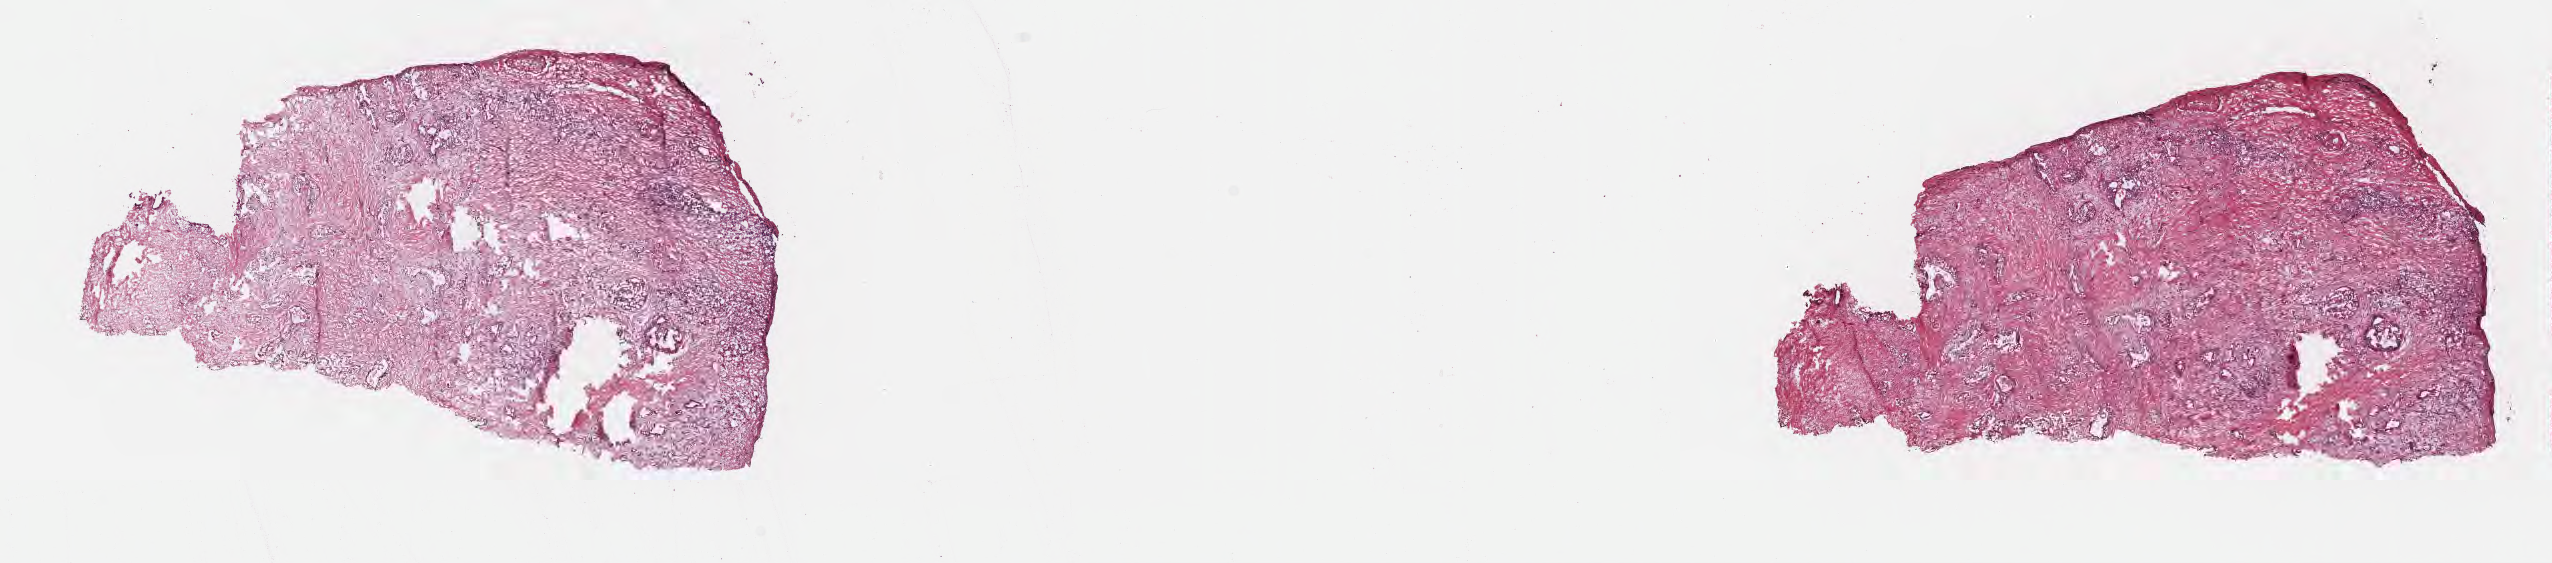
Whole-slide image, hematoxylin and eosin (H&E) stain, whole scanned area (about 20.6 x 4.6 mm) shown as a low-resolution overview, frozen section (tissue freezing medium), primary tumor, anatomic site: tail of pancreas. Female, age 63 years at initial diagnosis. Tumor grade: G2 (moderately differentiated). Composition of this section per pathologist review: tumor cells 20%, tumor nuclei 25%, stromal cells 80%, necrosis 0%, normal cells 0%. Inflammatory infiltration, as recorded: lymphocyte infiltration 0%, monocyte infiltration 0%, neutrophil infiltration 0%.
- histologic diagnosis: Infiltrating duct carcinoma, NOS
- AJCC pathologic stage: Stage III